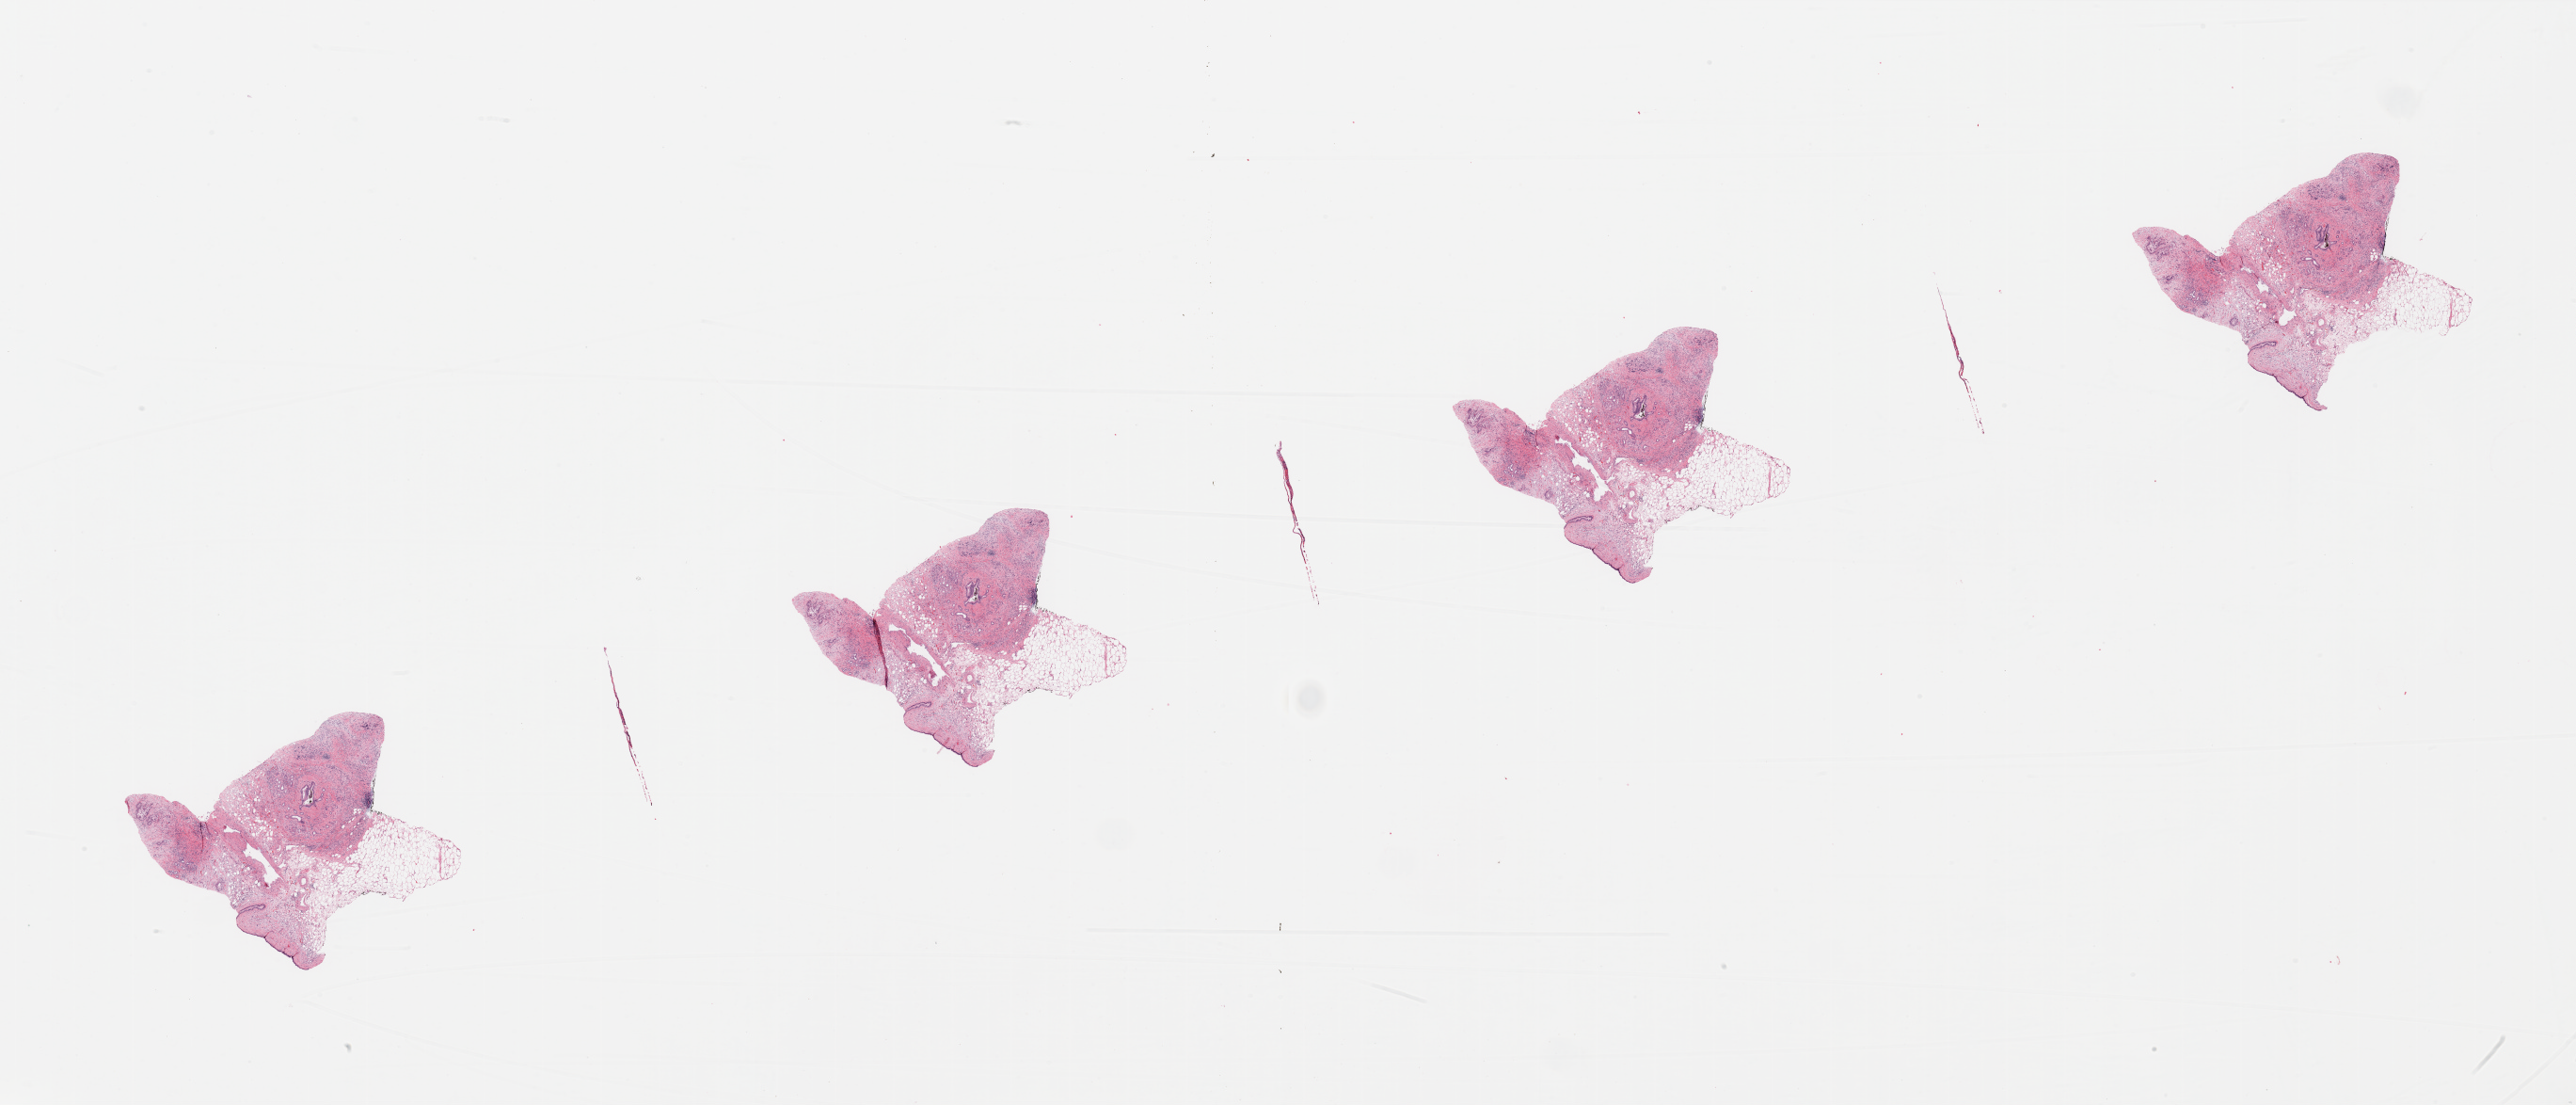
H&E whole-slide image, a low-resolution overview of the entire scanned area, about 43.3 x 18.6 mm. Tumour tissue sample, pancreas. 71-year-old male patient. Histologic grade: G2 (moderately differentiated).
Primary tumour site (as recorded): head. Histologic diagnosis: Infiltrating duct carcinoma, NOS. AJCC pathologic stage: IIB.